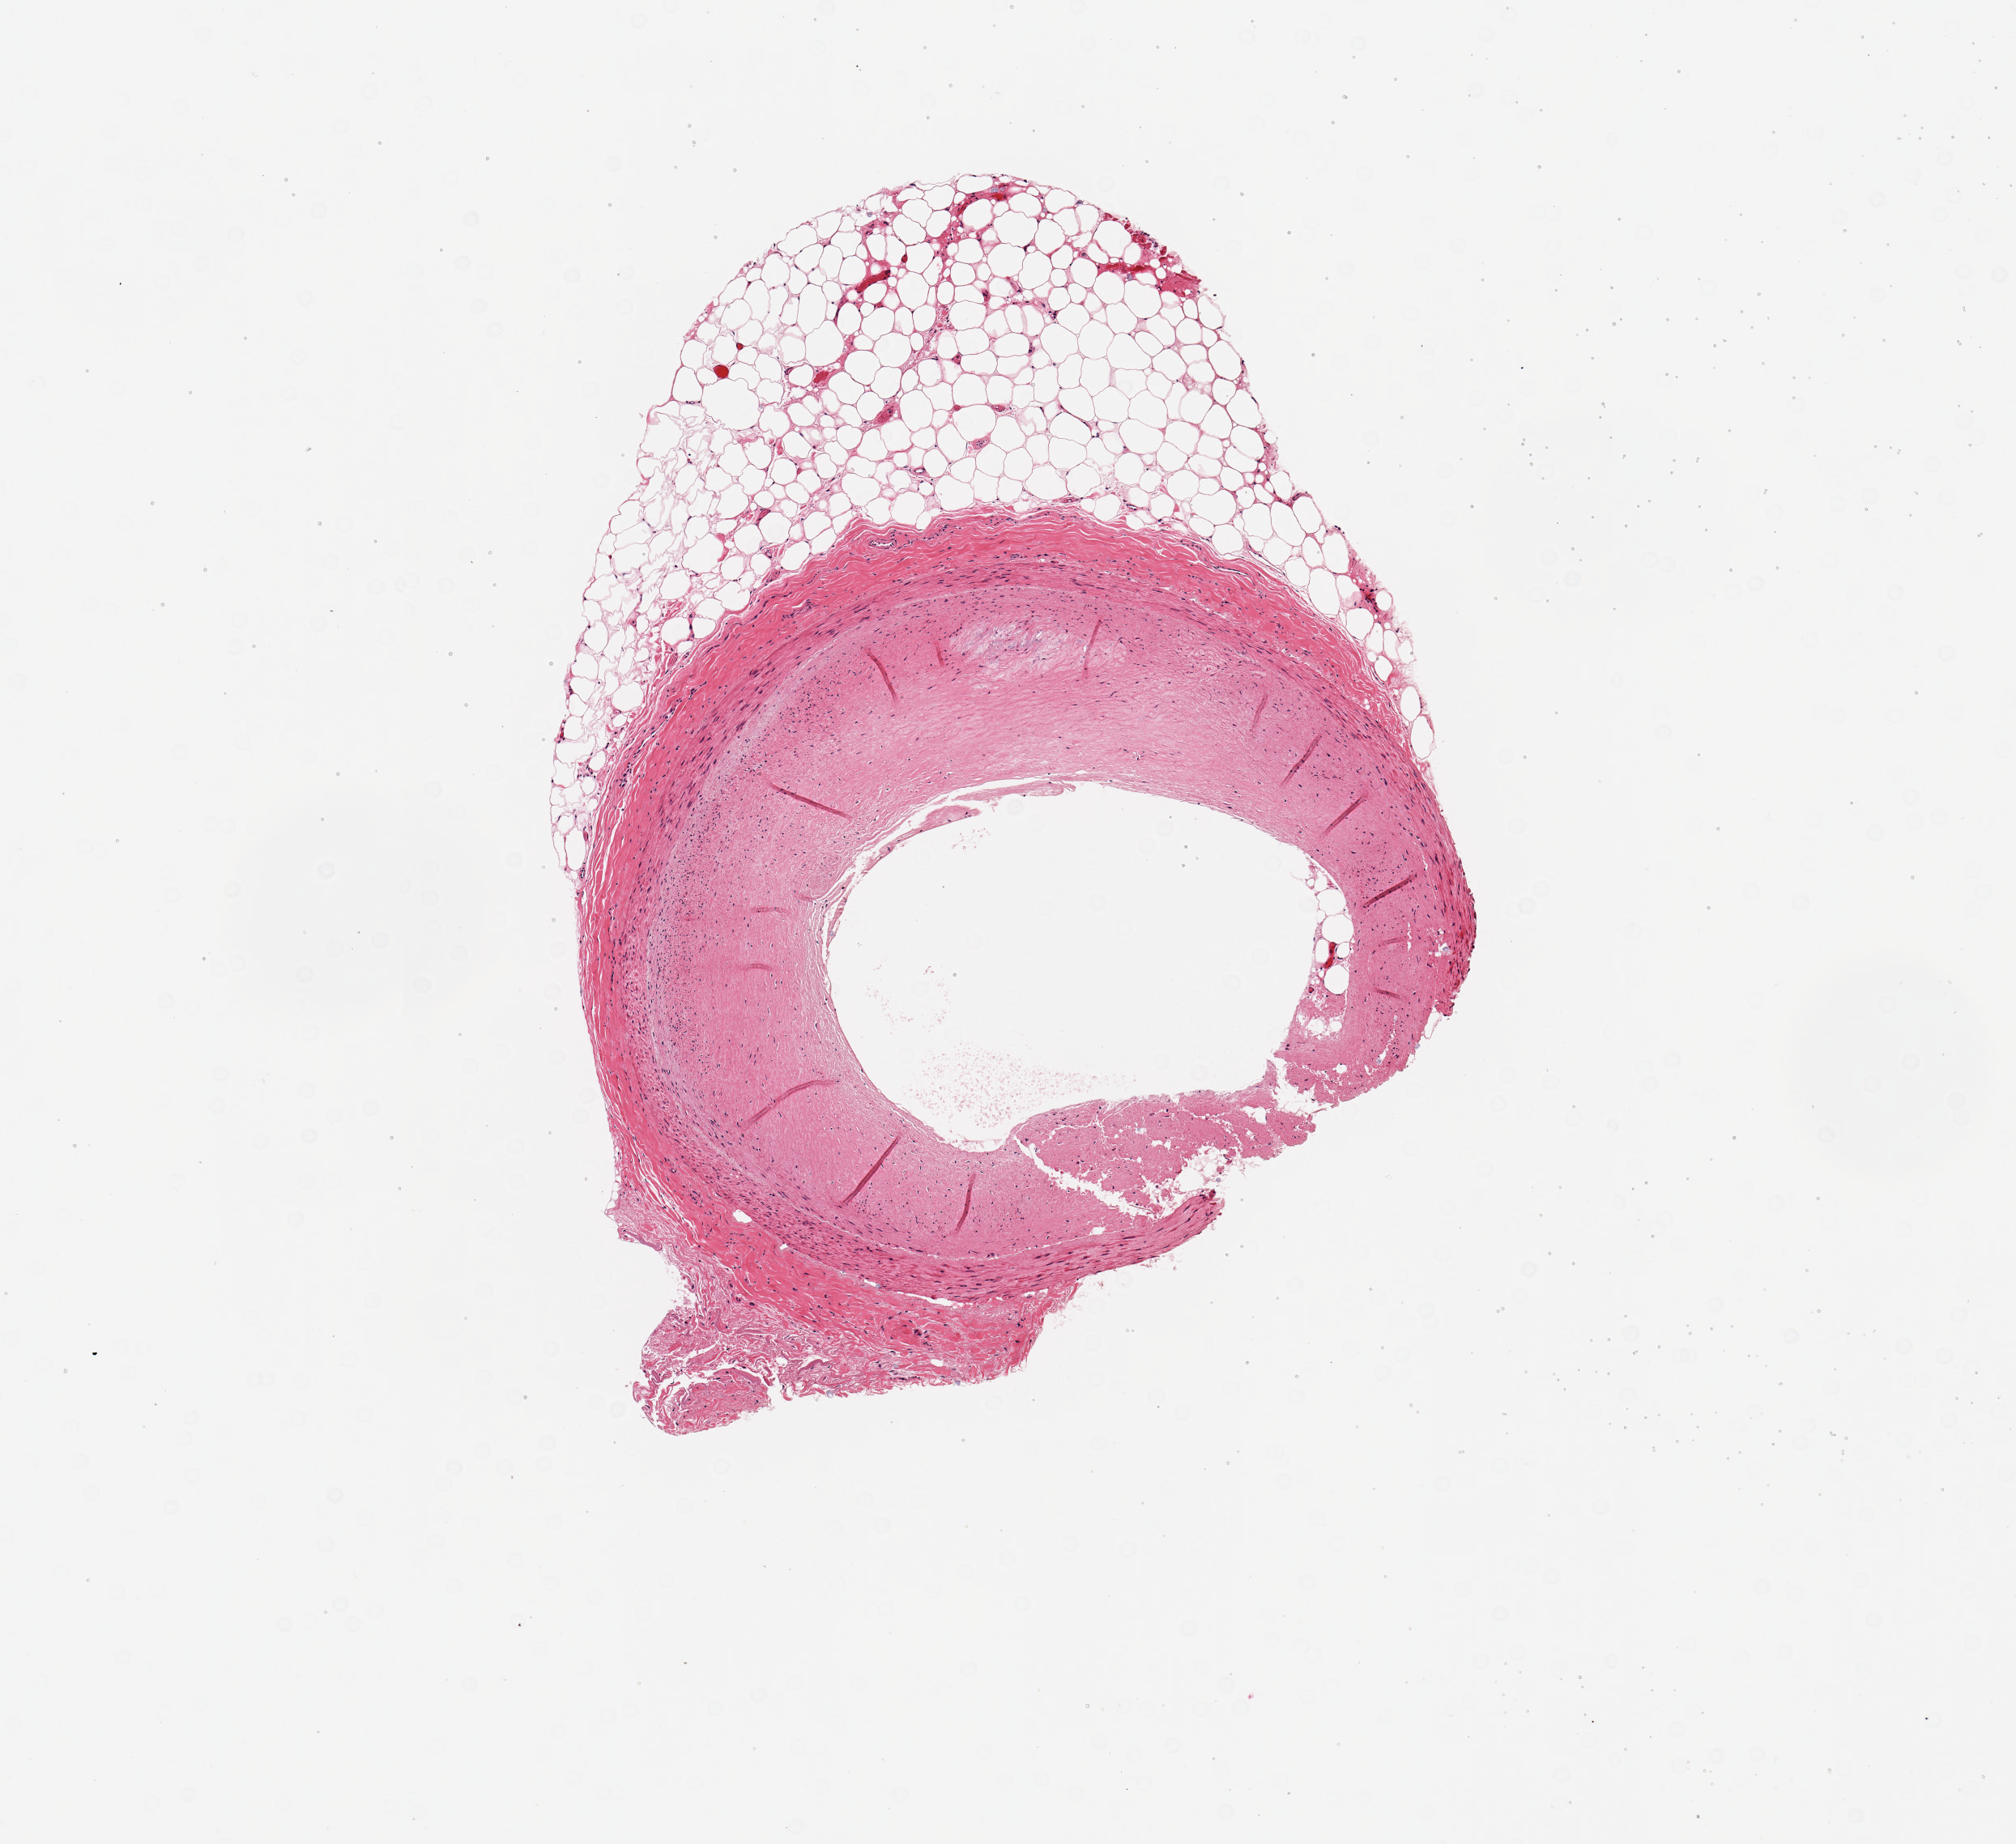
Whole-slide image, H&E stain, shown as a low-resolution overview of the whole scanned area (about 4.9 x 4.5 mm, from a 20x scan). PAXgene-fixed paraffin-embedded (PFPE) section. Target tissue: coronary artery. Tissue donor sample.
Pathologist's review note for this sample: 1 piece, atherosclerosis with narrowing of the lumen by ~50%, attached portion of fat (~30%).